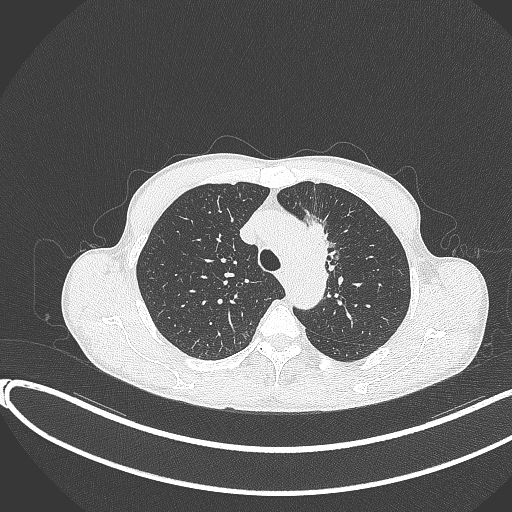
Chest CT, one axial slice; position 286 of 374 along the scan axis; reconstruction kernel B70f; lung window (W 1500 / L -600 HU); 512 × 512 image matrix, field of view 400 × 400 mm. Male patient, age 58 years. From the clinical record (not read from this slice): clinical TNM (as recorded): T1c N1 M0.
Outlined on this slice (rectangle marked by the reading radiologist):
- lung tumour (recorded histology: adenocarcinoma): bounding box <308,219,351,282> (left, top, right, bottom; pixels)